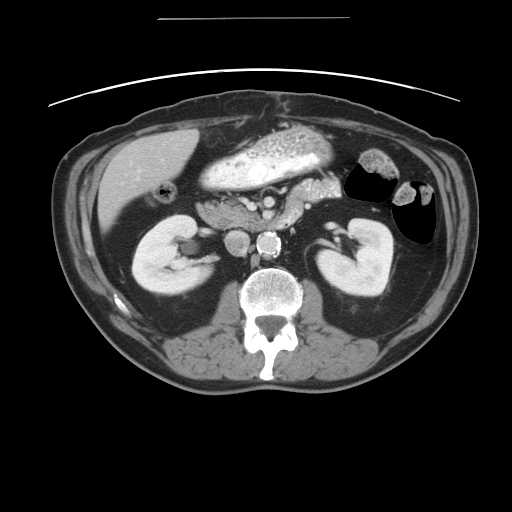
Contrast-enhanced abdominal CT, one axial slice. Position 17 of 49 along the scan axis. Reconstruction kernel STANDARD. Intravenous contrast given. Soft-tissue window (W 400 / L 40 HU). 512 × 512 image matrix. Male patient, age 57 years. From the clinical record (not read from this slice): diagnosis: colorectal cancer liver metastases, imaged before liver resection; multiple liver metastases: yes; largest metastasis: 4 cm; disease in both lobes: no.
Outlined on this slice (manually delineated by an expert):
- liver: bounding box (x1, y1, x2, y2) in pixels: (98, 129, 200, 231)